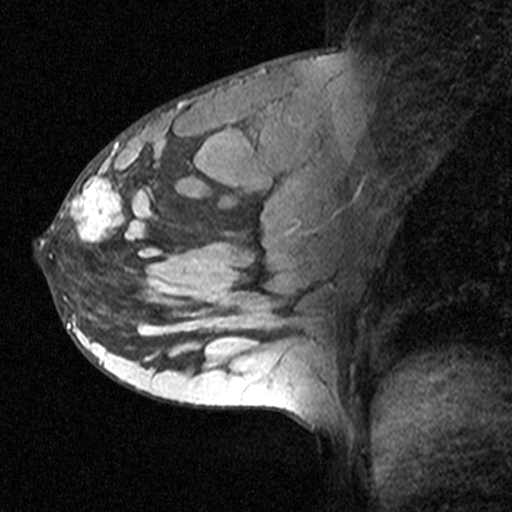
Breast MRI (dynamic contrast-enhanced), one sagittal slice; position 23 of 44 along the scan axis; dynamic contrast-enhanced study with each time point stored as its own series, time point 2 of 3 at this slice position (early post-contrast, ordered by acquisition time); 1.5 T; TE 4.5 ms, TR 11 ms; 3 mm slice thickness; 512 × 512 image matrix, field of view 200 × 200 mm. Female patient, age 27 years. From the clinical record (not read from this slice): setting: breast cancer imaged before/during neoadjuvant chemotherapy; receptor status: HR-positive, HER2-negative.
Annotated regions visible in this slice (semi-automatic segmentation, software-assisted and operator-edited):
- analysis volume of interest (the breast-tissue region the enhancement analysis was run in; not a lesion): box from (x=40, y=162) to (x=163, y=271) px
- tumour enhancement mask (voxels above the 90 % enhancement threshold inside the analysis volume of interest): (x=61, y=163)–(x=132, y=243)